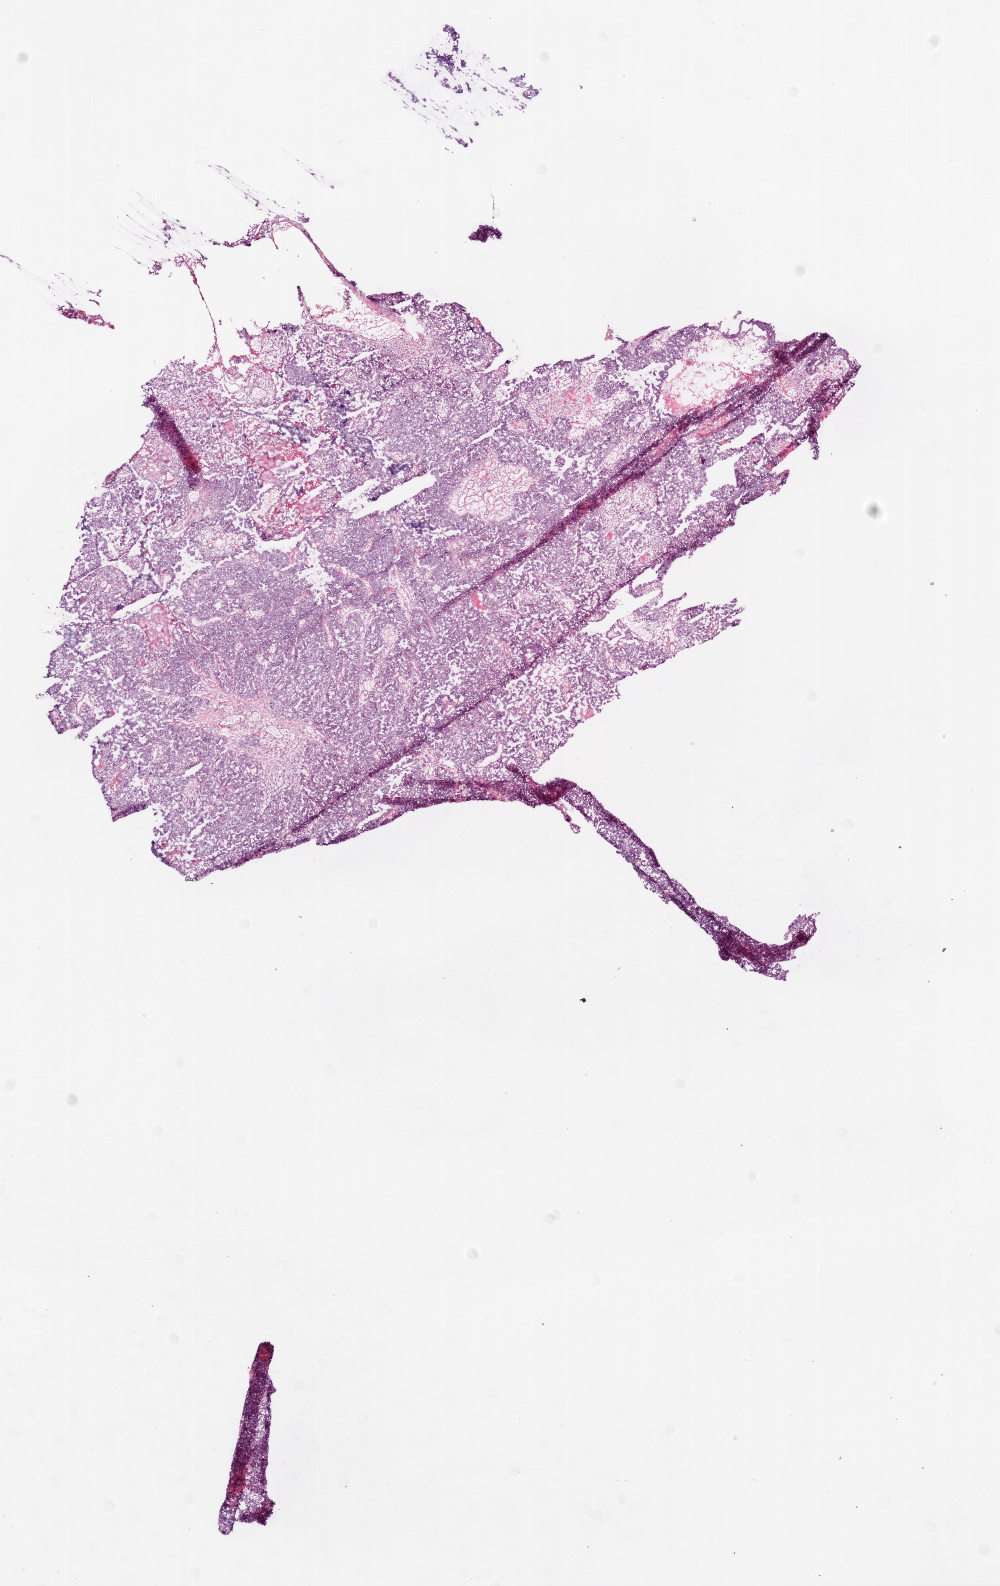
Hematoxylin and eosin (H&E) stained whole-slide image — shown as a low-resolution overview of the whole scanned area (about 8.0 x 12.7 mm, acquisition: 20x scan); frozen section from the top of the tissue portion; primary tumour sample from the ovary. Female patient; age at initial diagnosis 57 years. Histologic grade: G3 (poorly differentiated). Slide review estimates, as recorded: tumour cells 85%, tumour nuclei 95%, normal cells 0%, stromal cells 10%, necrosis 5%.
* pathologic diagnosis: Serous cystadenocarcinoma, NOS
* FIGO stage: IIIC